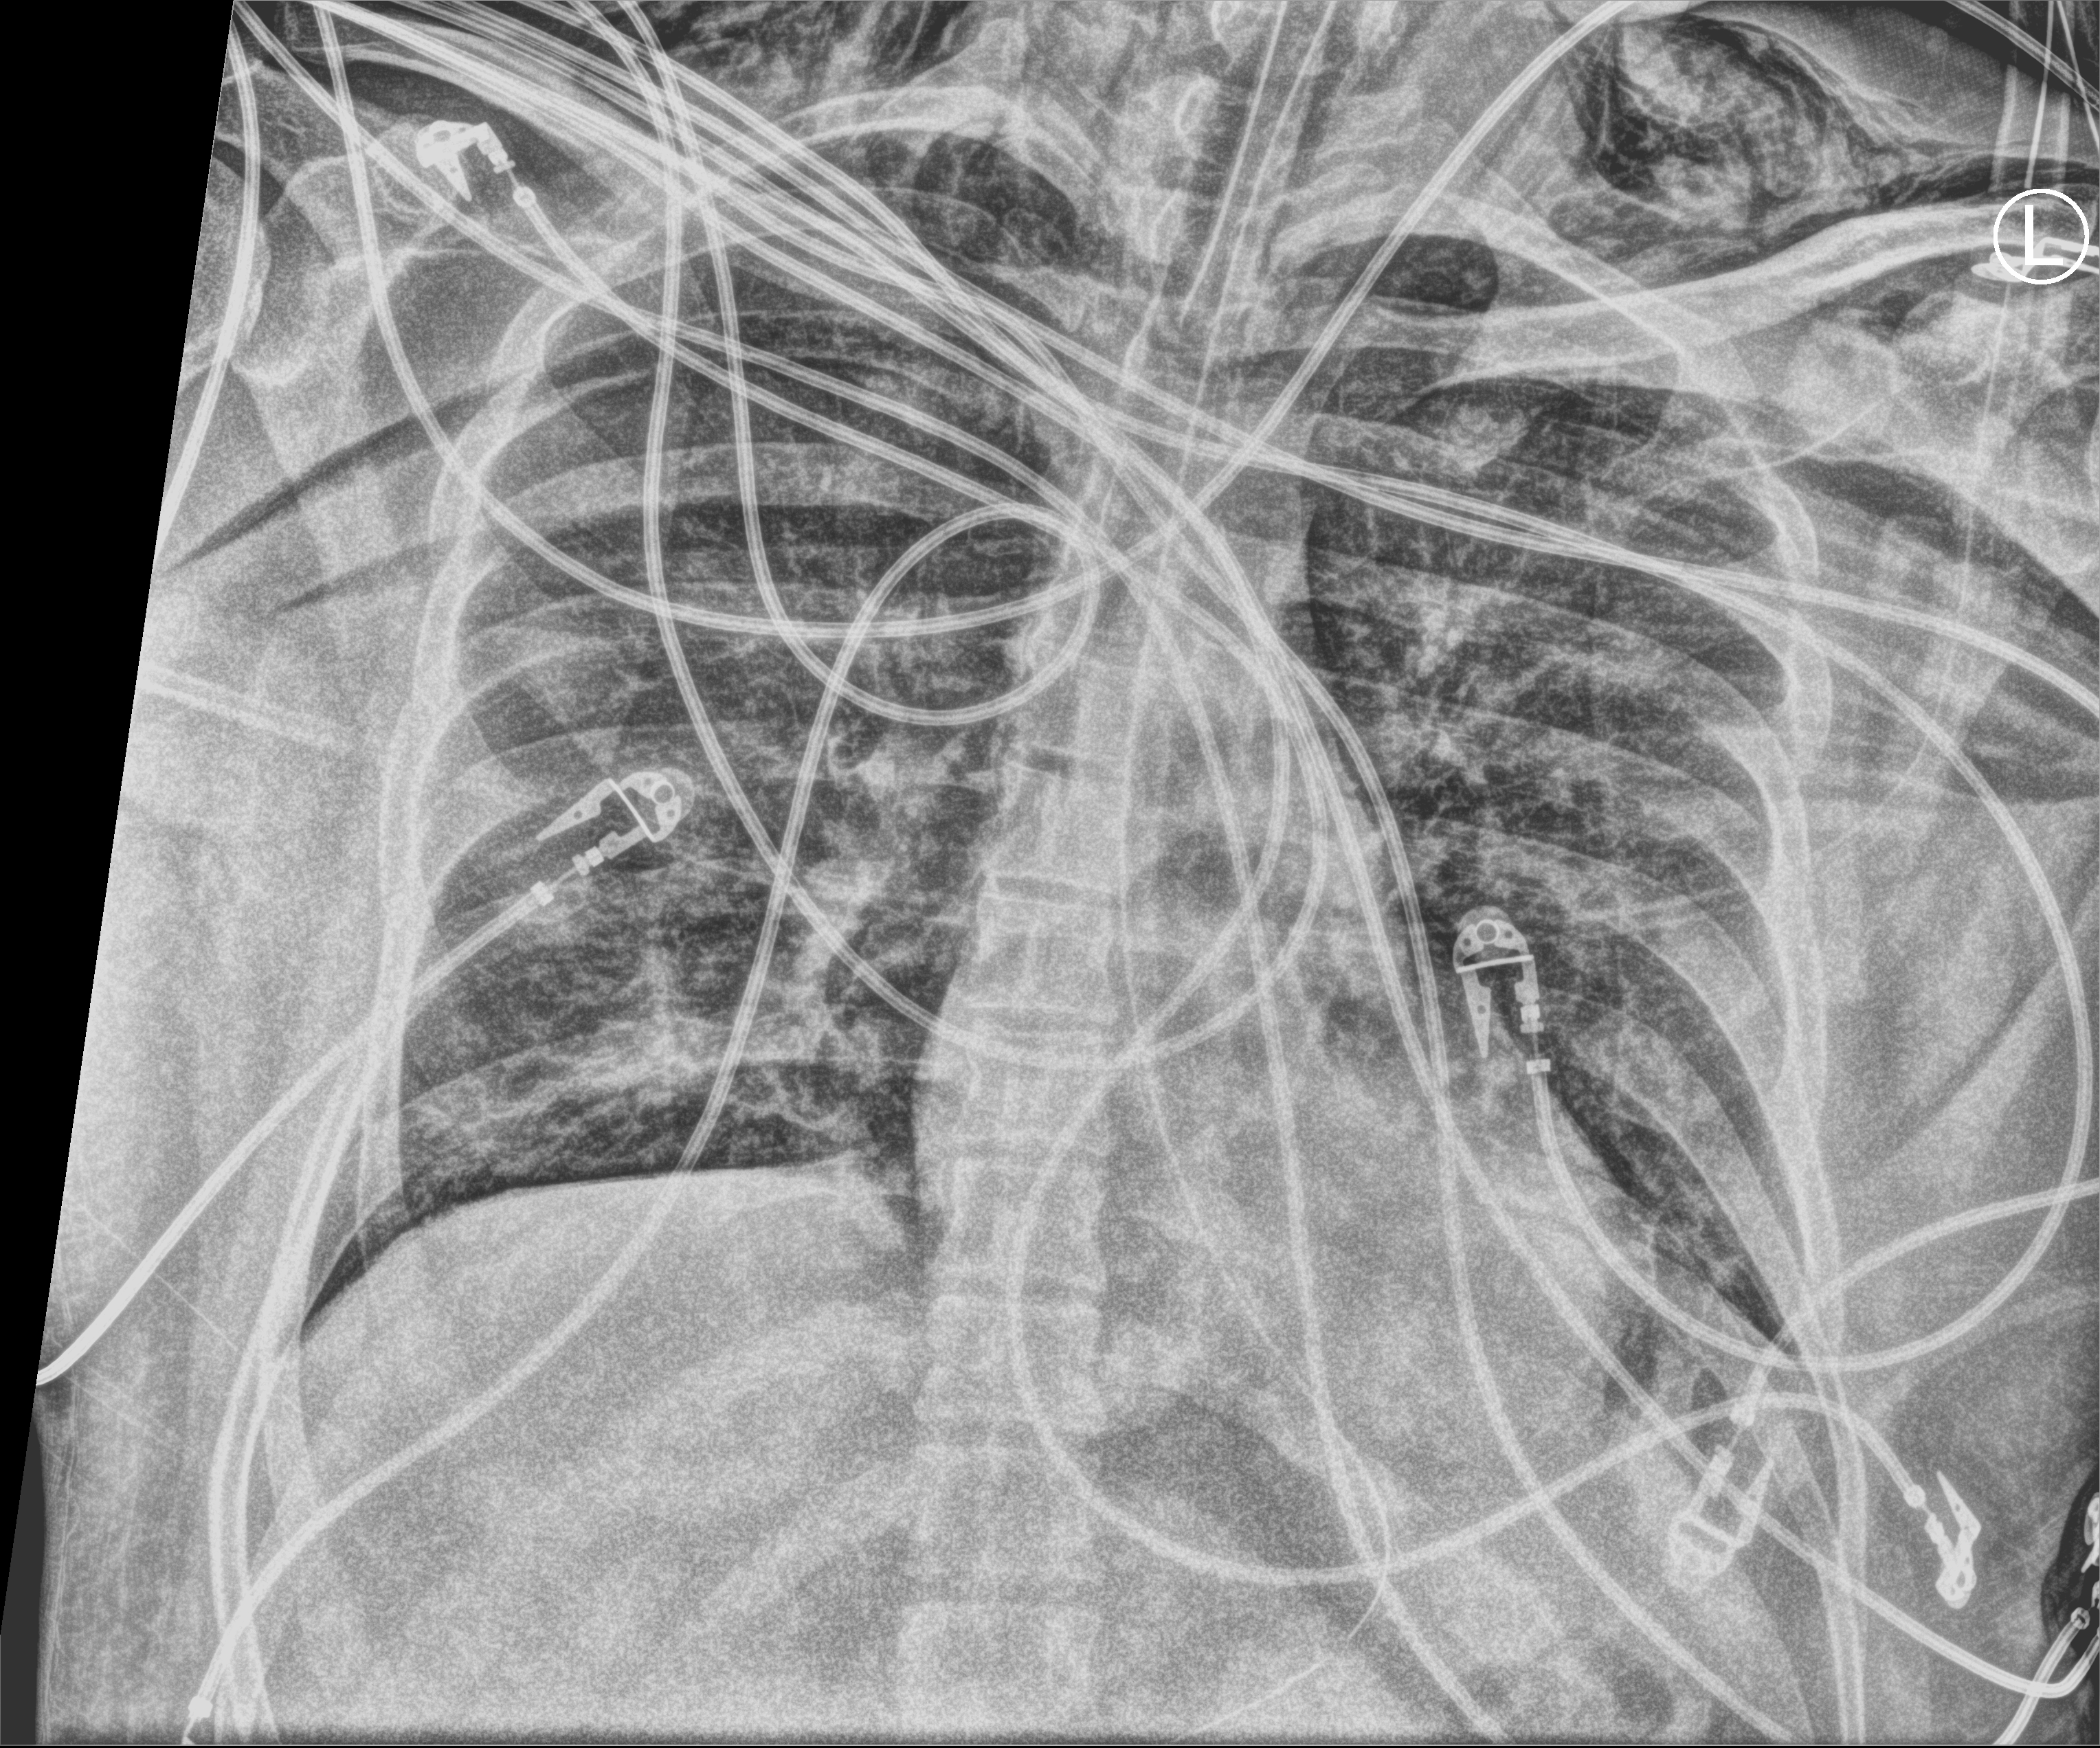
Bedside chest radiograph (computed radiography); anteroposterior (AP) projection. Patient hospitalised with COVID-19; male, aged 18–59 years.
Hospital-stay facts (about this admission, not read from this image; timing relative to this image not recorded): other chronic lung disease (admission record): no; mechanically ventilated during this hospital stay: yes.